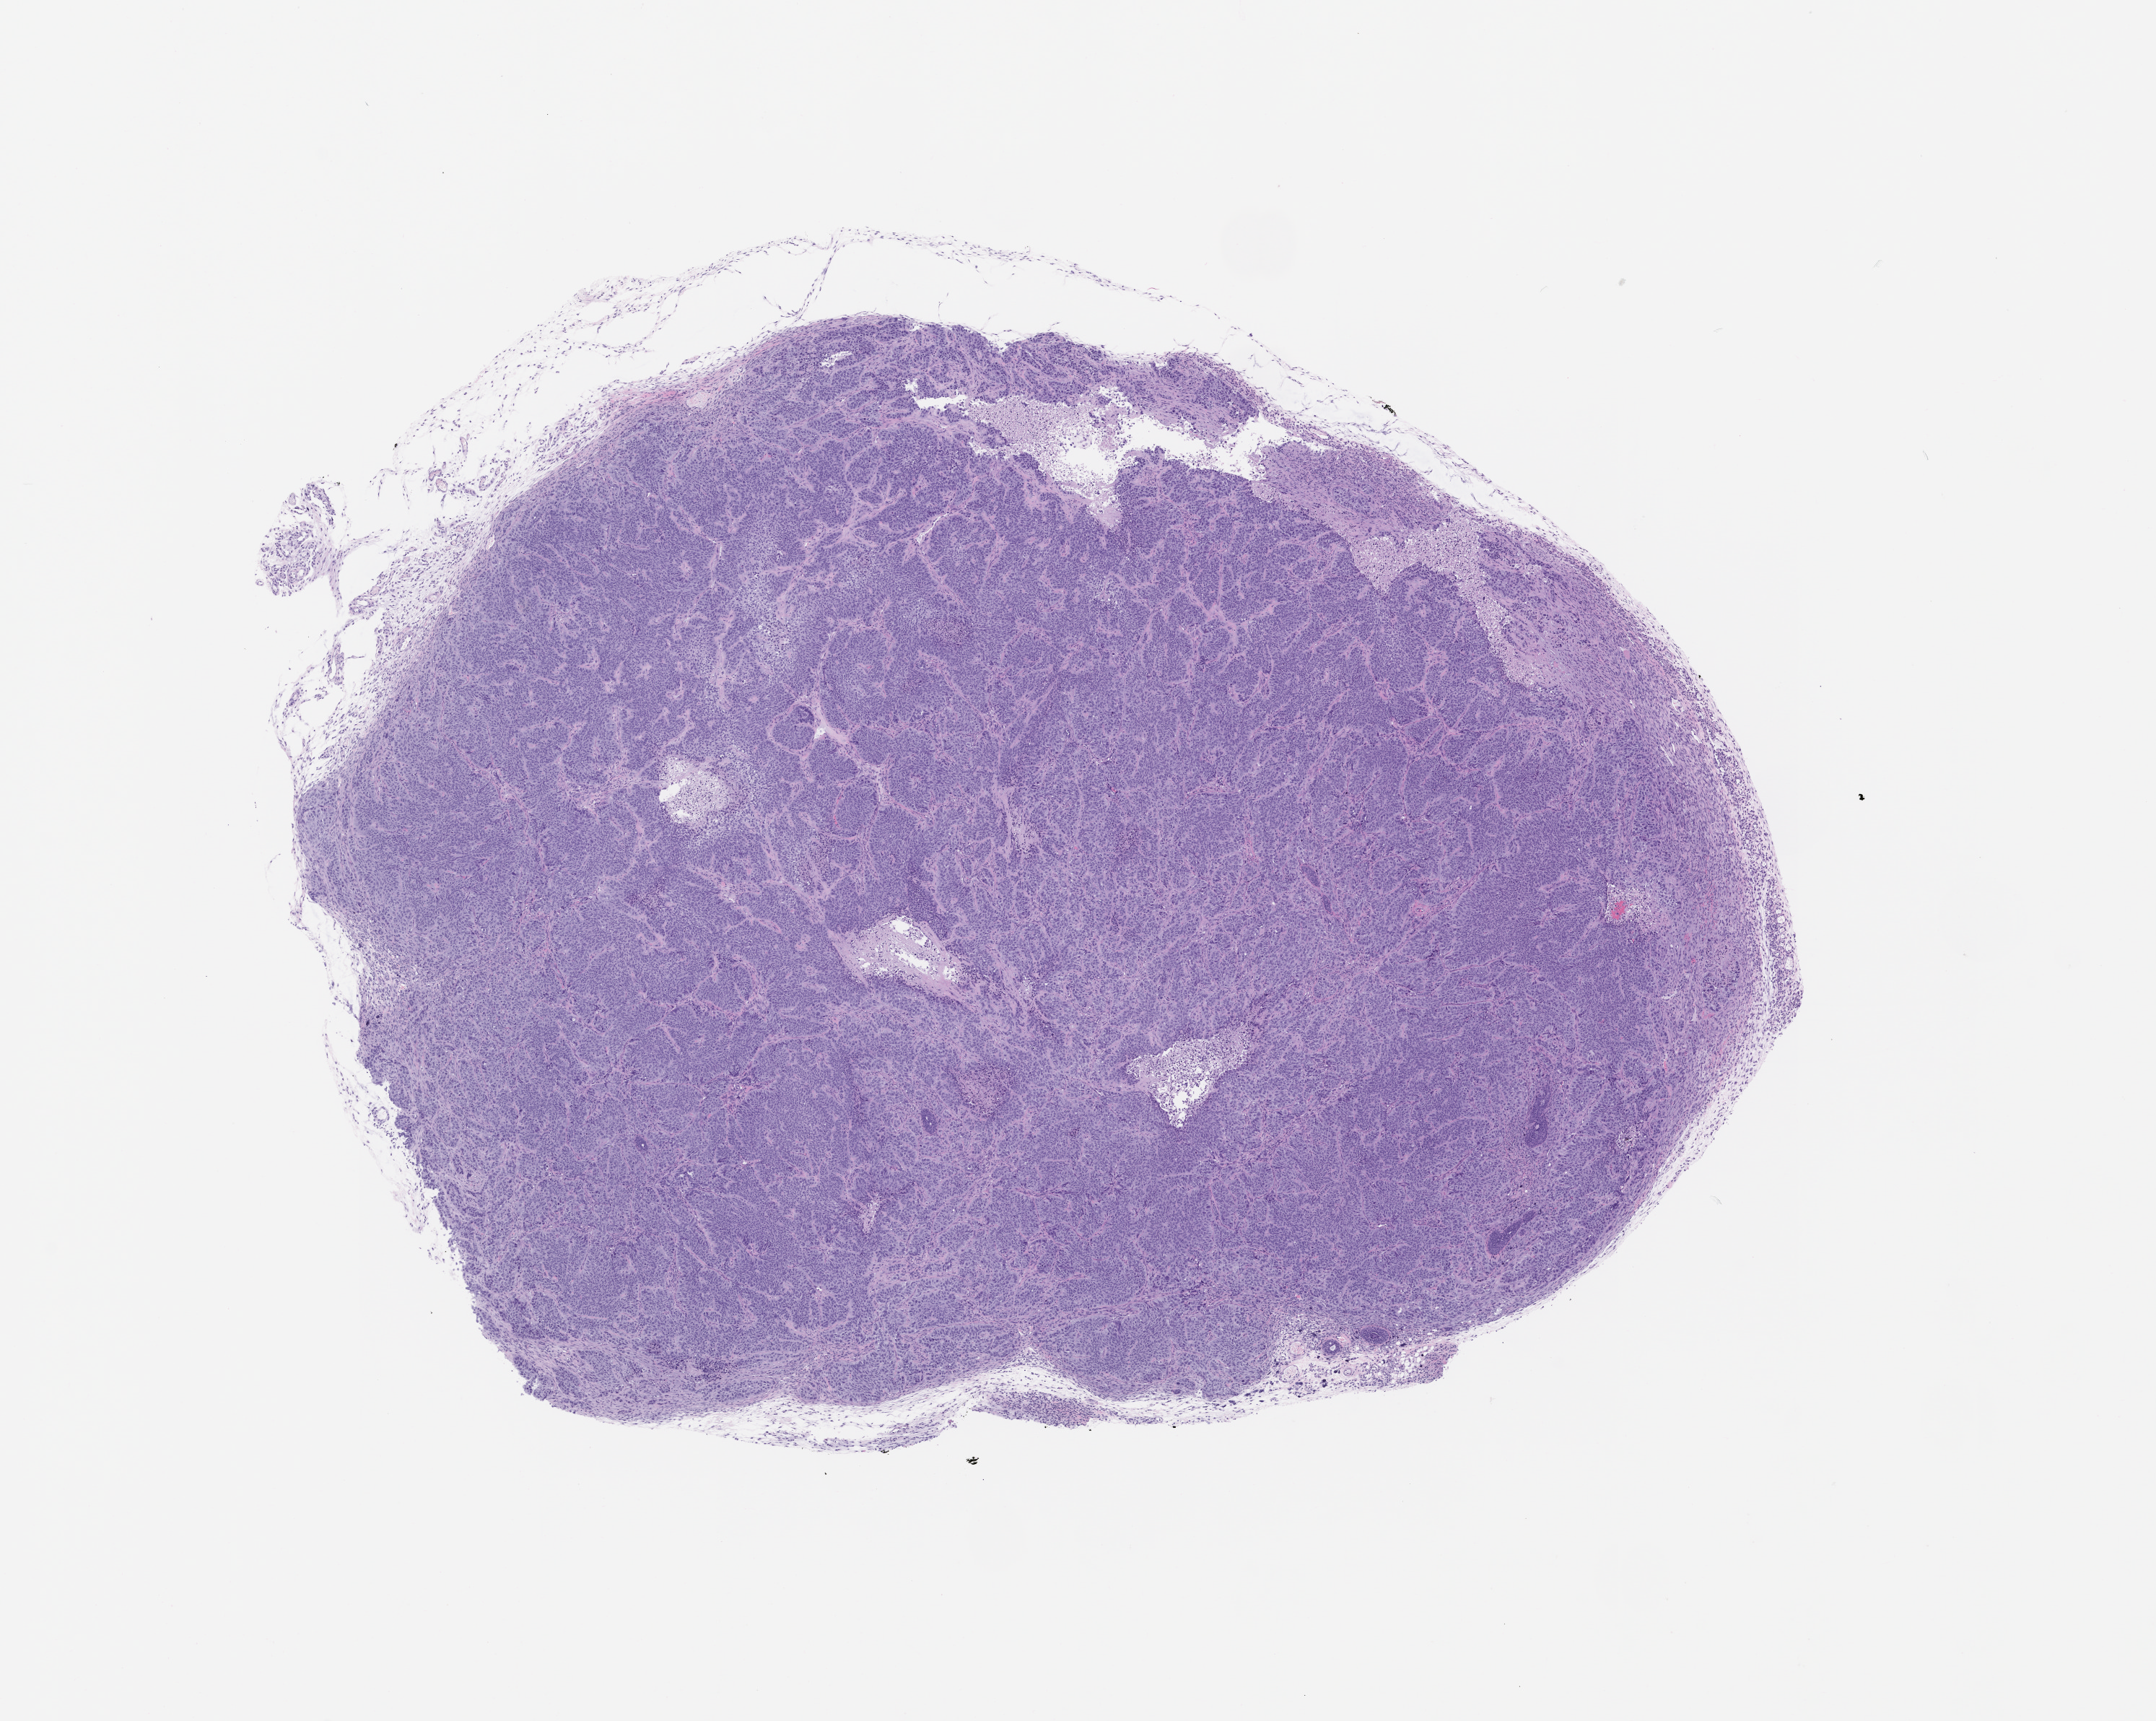
Haematoxylin and eosin whole-slide image of a patient-derived xenograft (PDX) tumor grown in a mouse, passage 0 — shown as a low-resolution overview of the whole scanned area (about 12.0 x 9.6 mm); formalin-fixed, paraffin-embedded (FFPE) tissue; tumor site category: lung.
Originating patient diagnosis: Lung Squamous Cell Carcinoma.